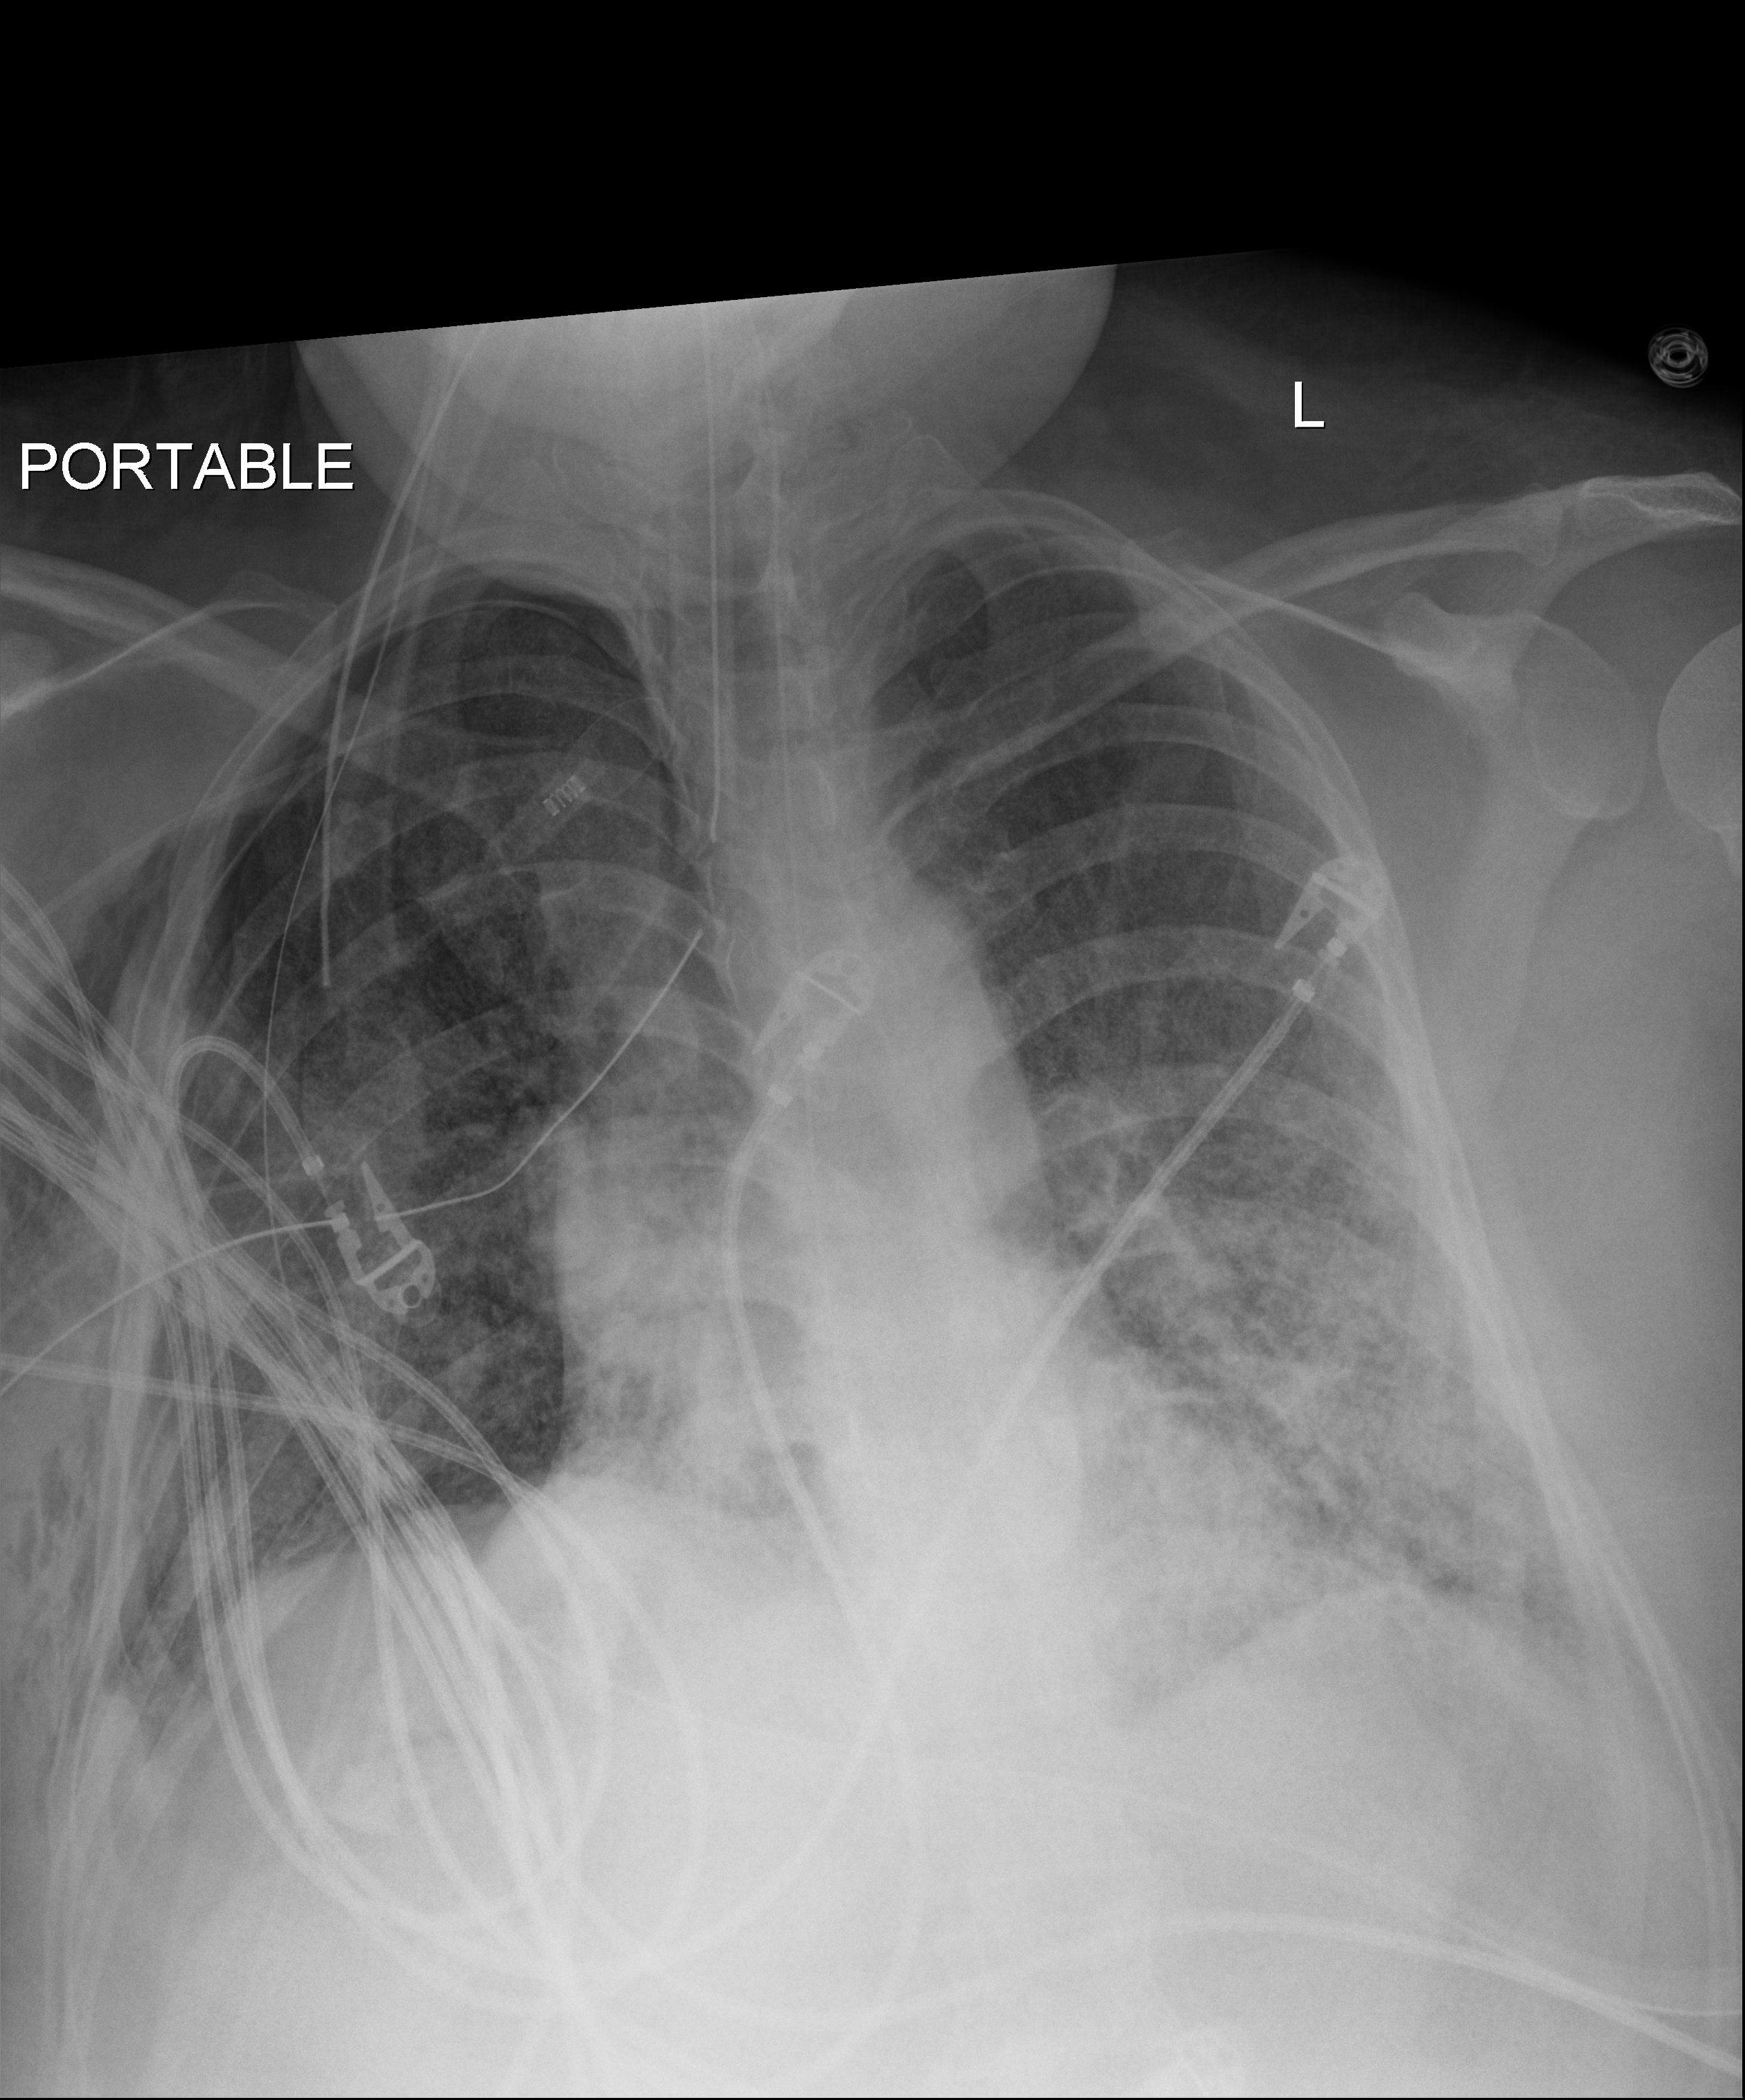
Portable chest radiograph, anteroposterior (AP) projection. Adult patient hospitalised with COVID-19, age 18–59 years.
From the hospital-stay record, not from the radiograph (when in the stay this image was taken is not recorded): smoking status (admission record): never.